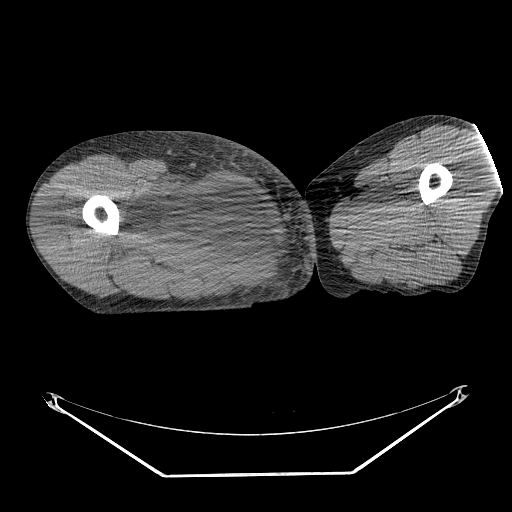
CT of an extremity soft-tissue mass (from a PET/CT study), one axial slice. Position 246 of 311 along the scan axis. Soft-tissue window (W 400 / L 40 HU). 3.75 mm slice thickness. 512 × 512 image matrix. Male patient. Case-level facts recorded for this patient, not image findings: histological type: undifferentiated - pleiomorphic; grade: high; site of the primary tumour: right thigh.
Structures marked on this image (expert contour drawn on MRI and transferred to this co-registered scan by the dataset authors):
- gross tumour volume including surrounding oedema: bounding box [x1, y1, x2, y2] px = [130, 174, 241, 255]
- gross tumour volume (mass): [158, 180, 239, 255]